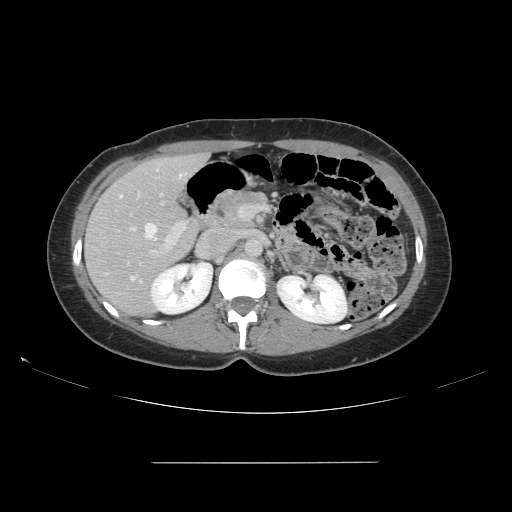
Contrast-enhanced abdominal CT, one axial slice. Intravenous contrast given. Soft-tissue window (W 400 / L 40 HU). 2.5 mm slice thickness. 512 × 512 image matrix, field of view 421 × 421 mm. Female patient, age 46 years. From the clinical record (not read from this slice): diagnosis: colorectal cancer liver metastases, imaged before liver resection; multiple liver metastases: yes; largest metastasis: 3 cm.
Structures marked on this image (outlined manually by an expert reader):
- hepatic veins: bounding box [x1, y1, x2, y2] px = [119, 174, 183, 279]
- liver: [85, 155, 207, 316]
- planned liver remnant (the part of the liver to remain after resection): [94, 155, 201, 312]
- portal vein (with intrahepatic branches): [129, 190, 246, 258]